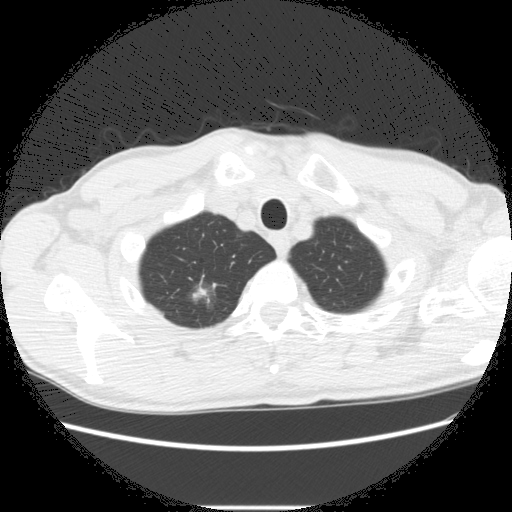
Axial slice from a low-dose chest CT screening exam. Second annual screen. Lung window (W 1500 / L -600 HU). 2.5 mm slice thickness. Standard (soft-tissue) reconstruction kernel (STANDARD). Slice 27 of 282 in the series. Male, age 66 years at enrolment.
Expert-annotated lung lesion, box from (x=172, y=279) to (x=231, y=326) px. The screening reader recorded 5 non-calcified nodules or masses ≥4 mm on this exam (right lower lobe, right upper lobe, right upper lobe, right upper lobe, left lower lobe); which of them this box marks is not recorded. Participant outcome: lung cancer diagnosed 75 days after this screen — adenocarcinoma, NOS, right upper lobe, undifferentiated (G4), stage IA (AJCC 6th edition), 20 mm at pathology.